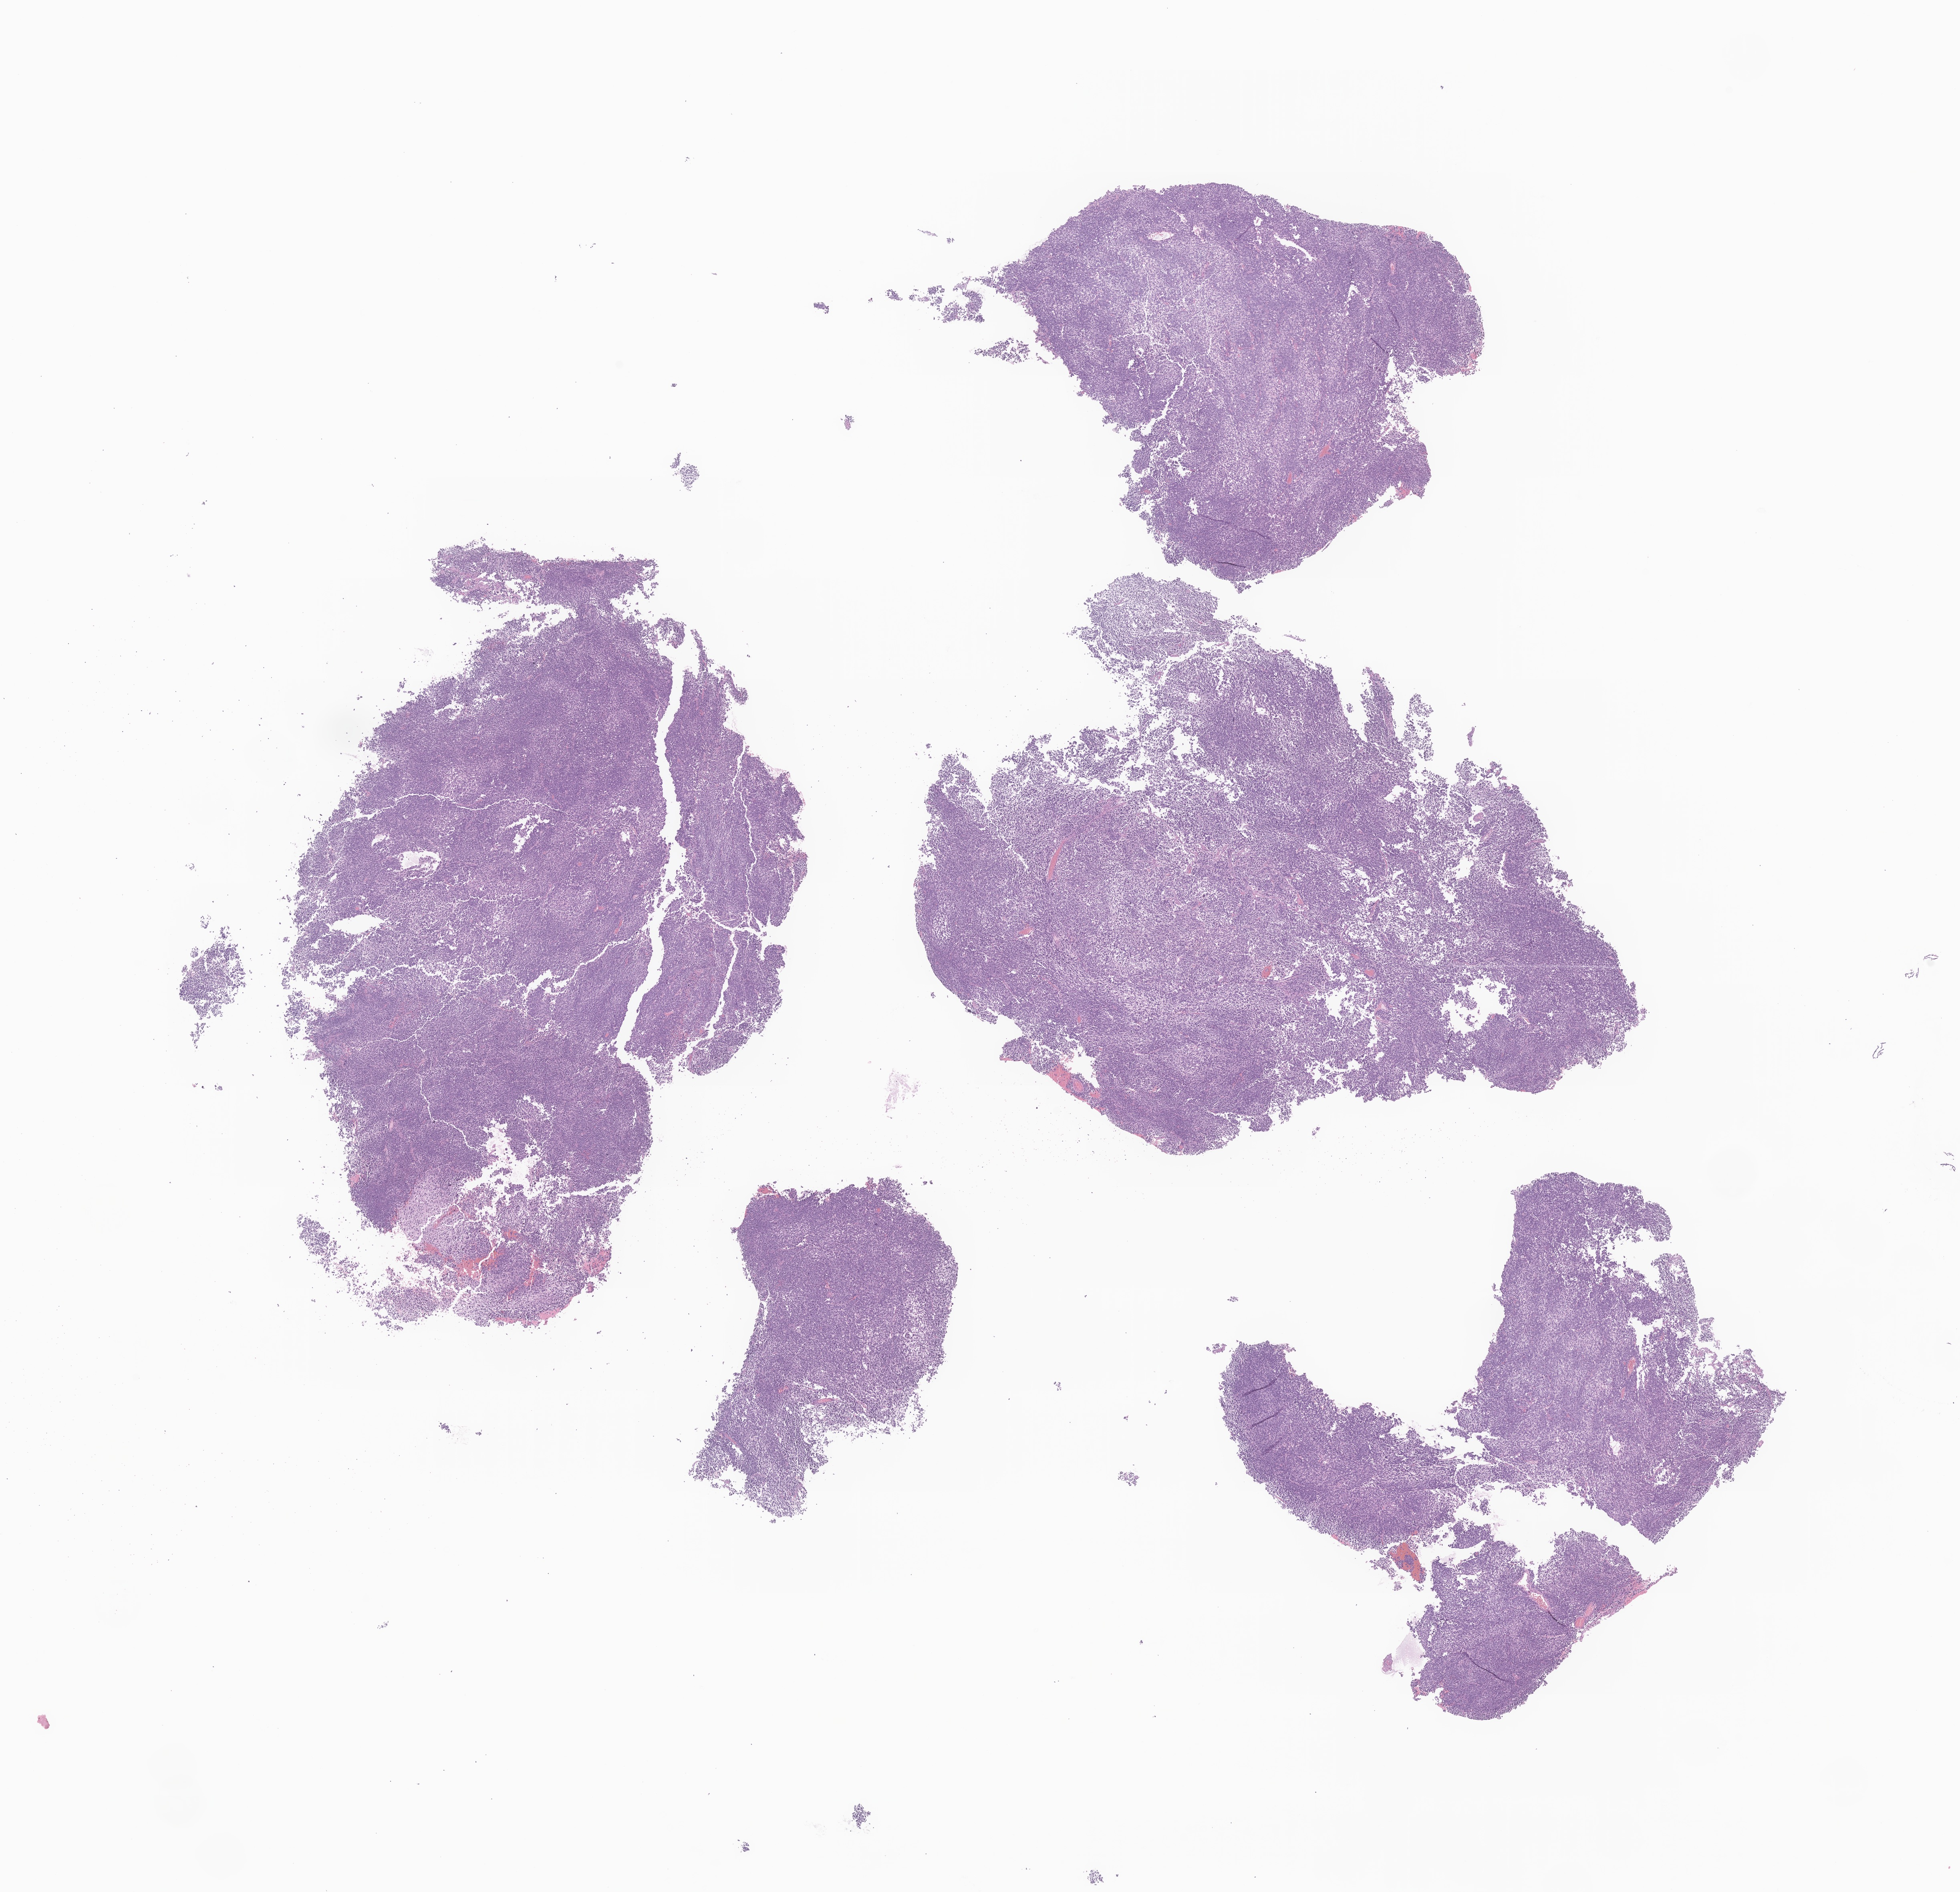
Haematoxylin and eosin whole-slide image of tumor tissue from the brain, whole scanned area (about 20.6 x 19.9 mm) shown as a low-resolution overview. Formalin-fixed paraffin-embedded section. Male patient, age 119 months (9 years 11 months).
Recorded diagnosis: Medulloblastoma, NOS.